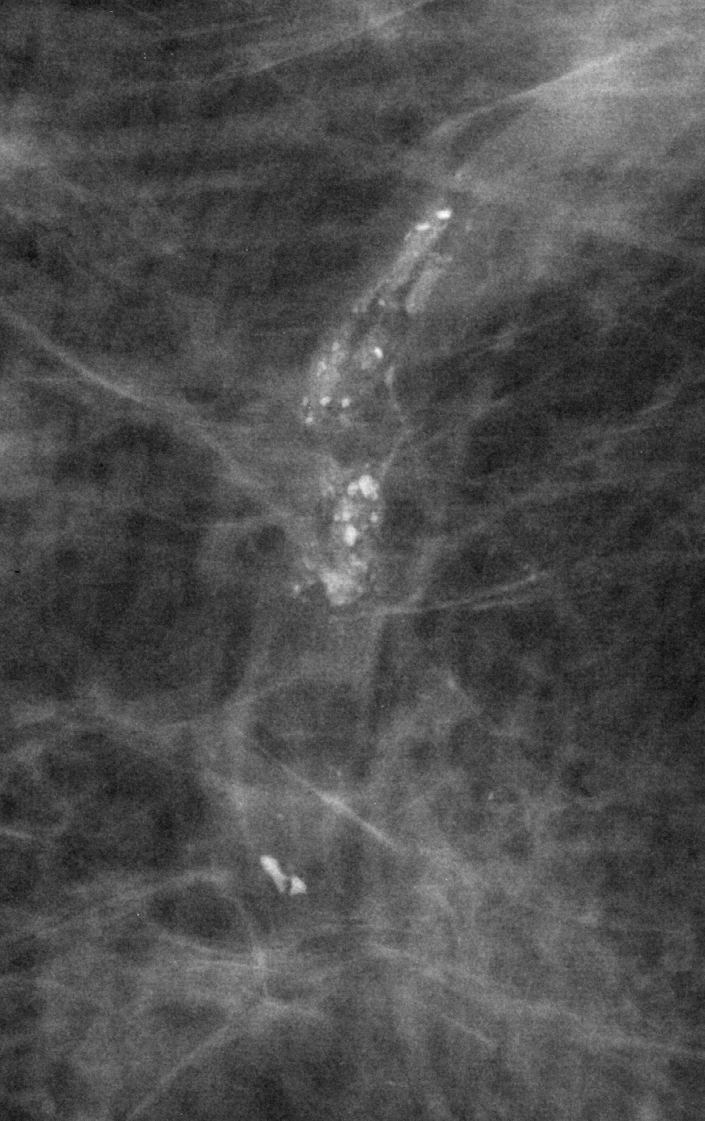
Crop from a digitized film mammogram around one marked abnormality, right breast, CC view.
- Calcifications, morphology pleomorphic, distribution segmental; BI-RADS assessment category 4; subtlety rating 5 on a 1 (subtle) to 5 (obvious) scale; pathology (as recorded): benign.